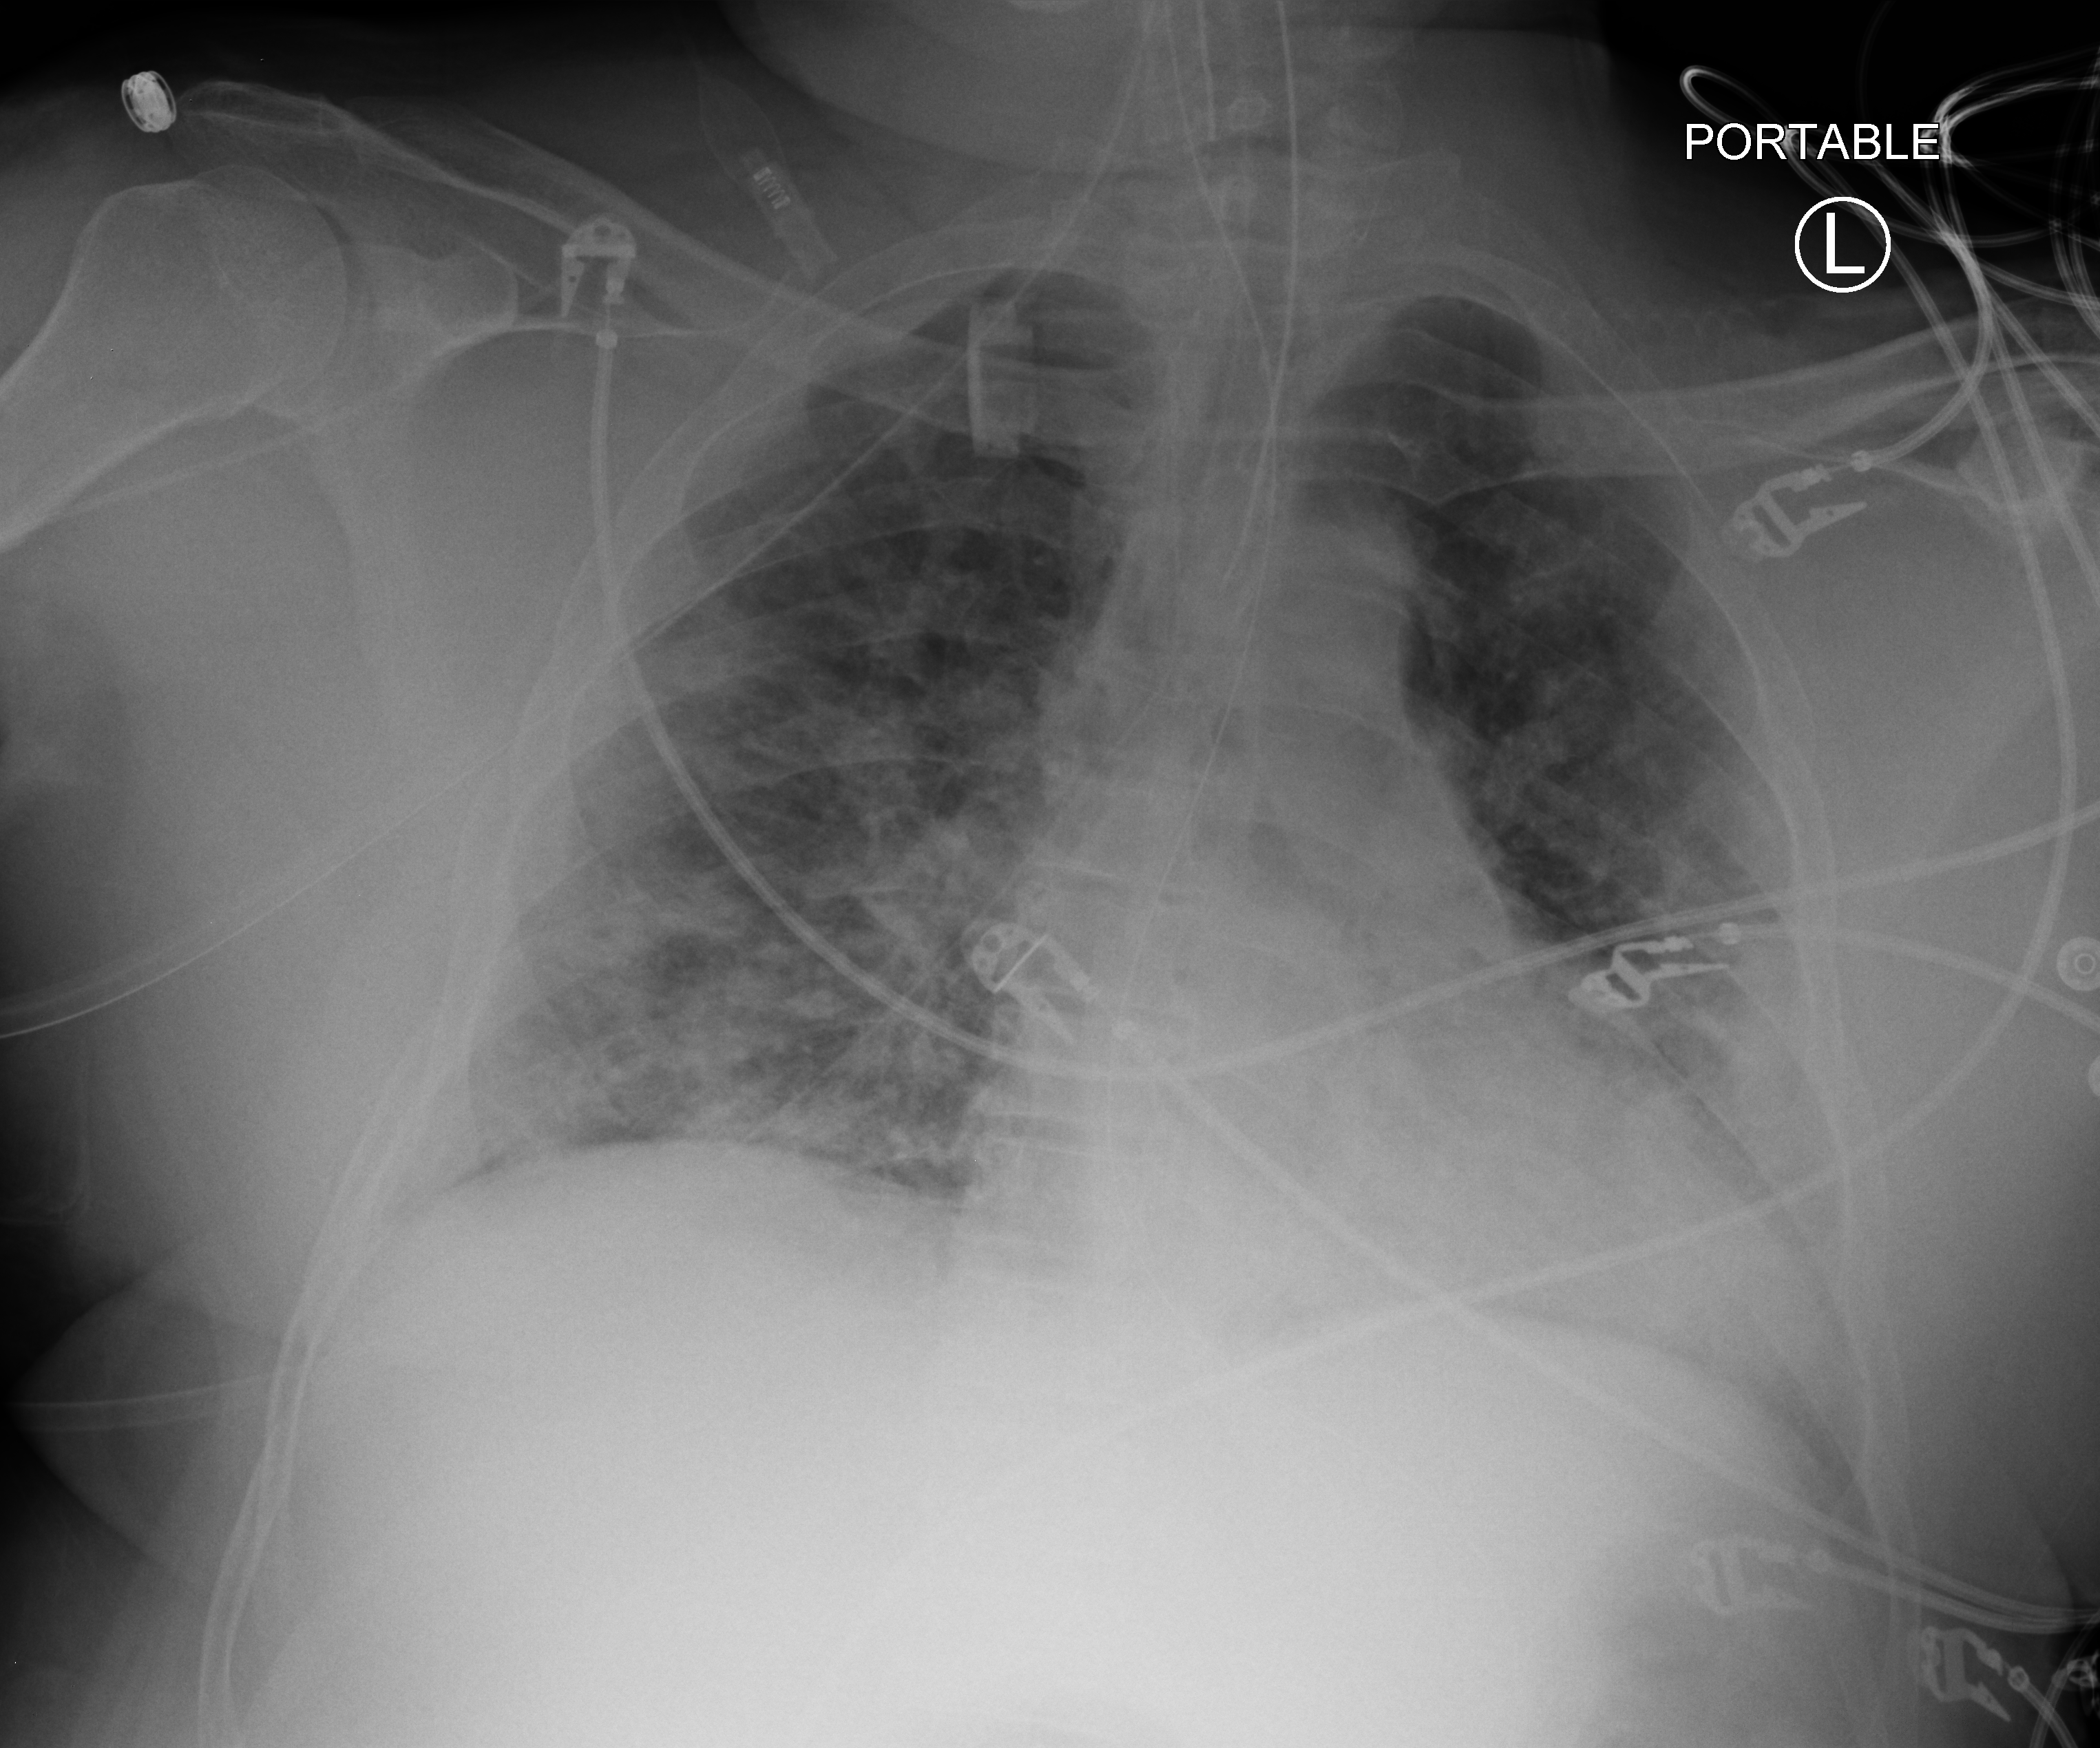
Chest X-ray (portable). Male patient hospitalised with COVID-19, age 18–59 years.
From the hospital-stay record, not from the radiograph (when in the stay this image was taken is not recorded): admitted to intensive care during this hospital stay: yes.